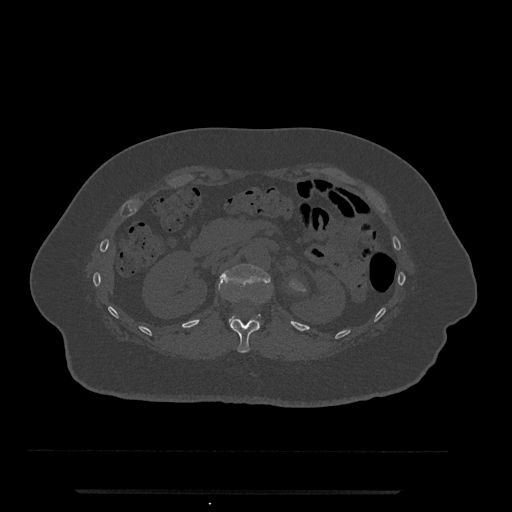
CT including the spine, one axial slice. Position 140 of 797 along the scan axis. Reconstruction kernel Br40s/3. Bone window (W 1800 / L 400 HU). 0.5 mm slice thickness. 512 × 512 image matrix, field of view 440 × 440 mm. Patient: female, 51 years. Case-level facts recorded for this patient, not image findings: primary cancer: neuro; vertebrae with lytic lesions (as recorded): T8.
Outlined on this slice (semi-automatically segmented with operator editing):
- L1 vertebra: bounding box (x1, y1, x2, y2) in pixels: (218, 264, 270, 327)
- T12 vertebra: (230, 318, 259, 353)